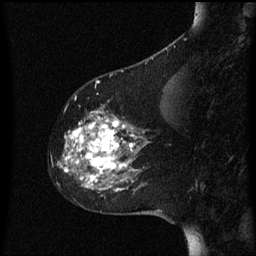
Breast MRI (dynamic contrast-enhanced), one sagittal slice; dynamic contrast-enhanced series, image 2 of 3 at this slice position (ordered by acquisition); 1.5 T; TE 4.2 ms, TR 8 ms; 2 mm slice thickness; 256 × 256 image matrix, field of view 200 × 200 mm. Patient: female, 60 years.
Annotated regions visible in this slice (semi-automatically segmented with operator editing):
- analysis volume of interest (the breast-tissue region the enhancement analysis was run in; not a lesion): box from (x=53, y=106) to (x=151, y=197) px
- tumour enhancement mask (voxels above the 70 % enhancement threshold inside the analysis volume of interest): (x=58, y=112)–(x=137, y=191)